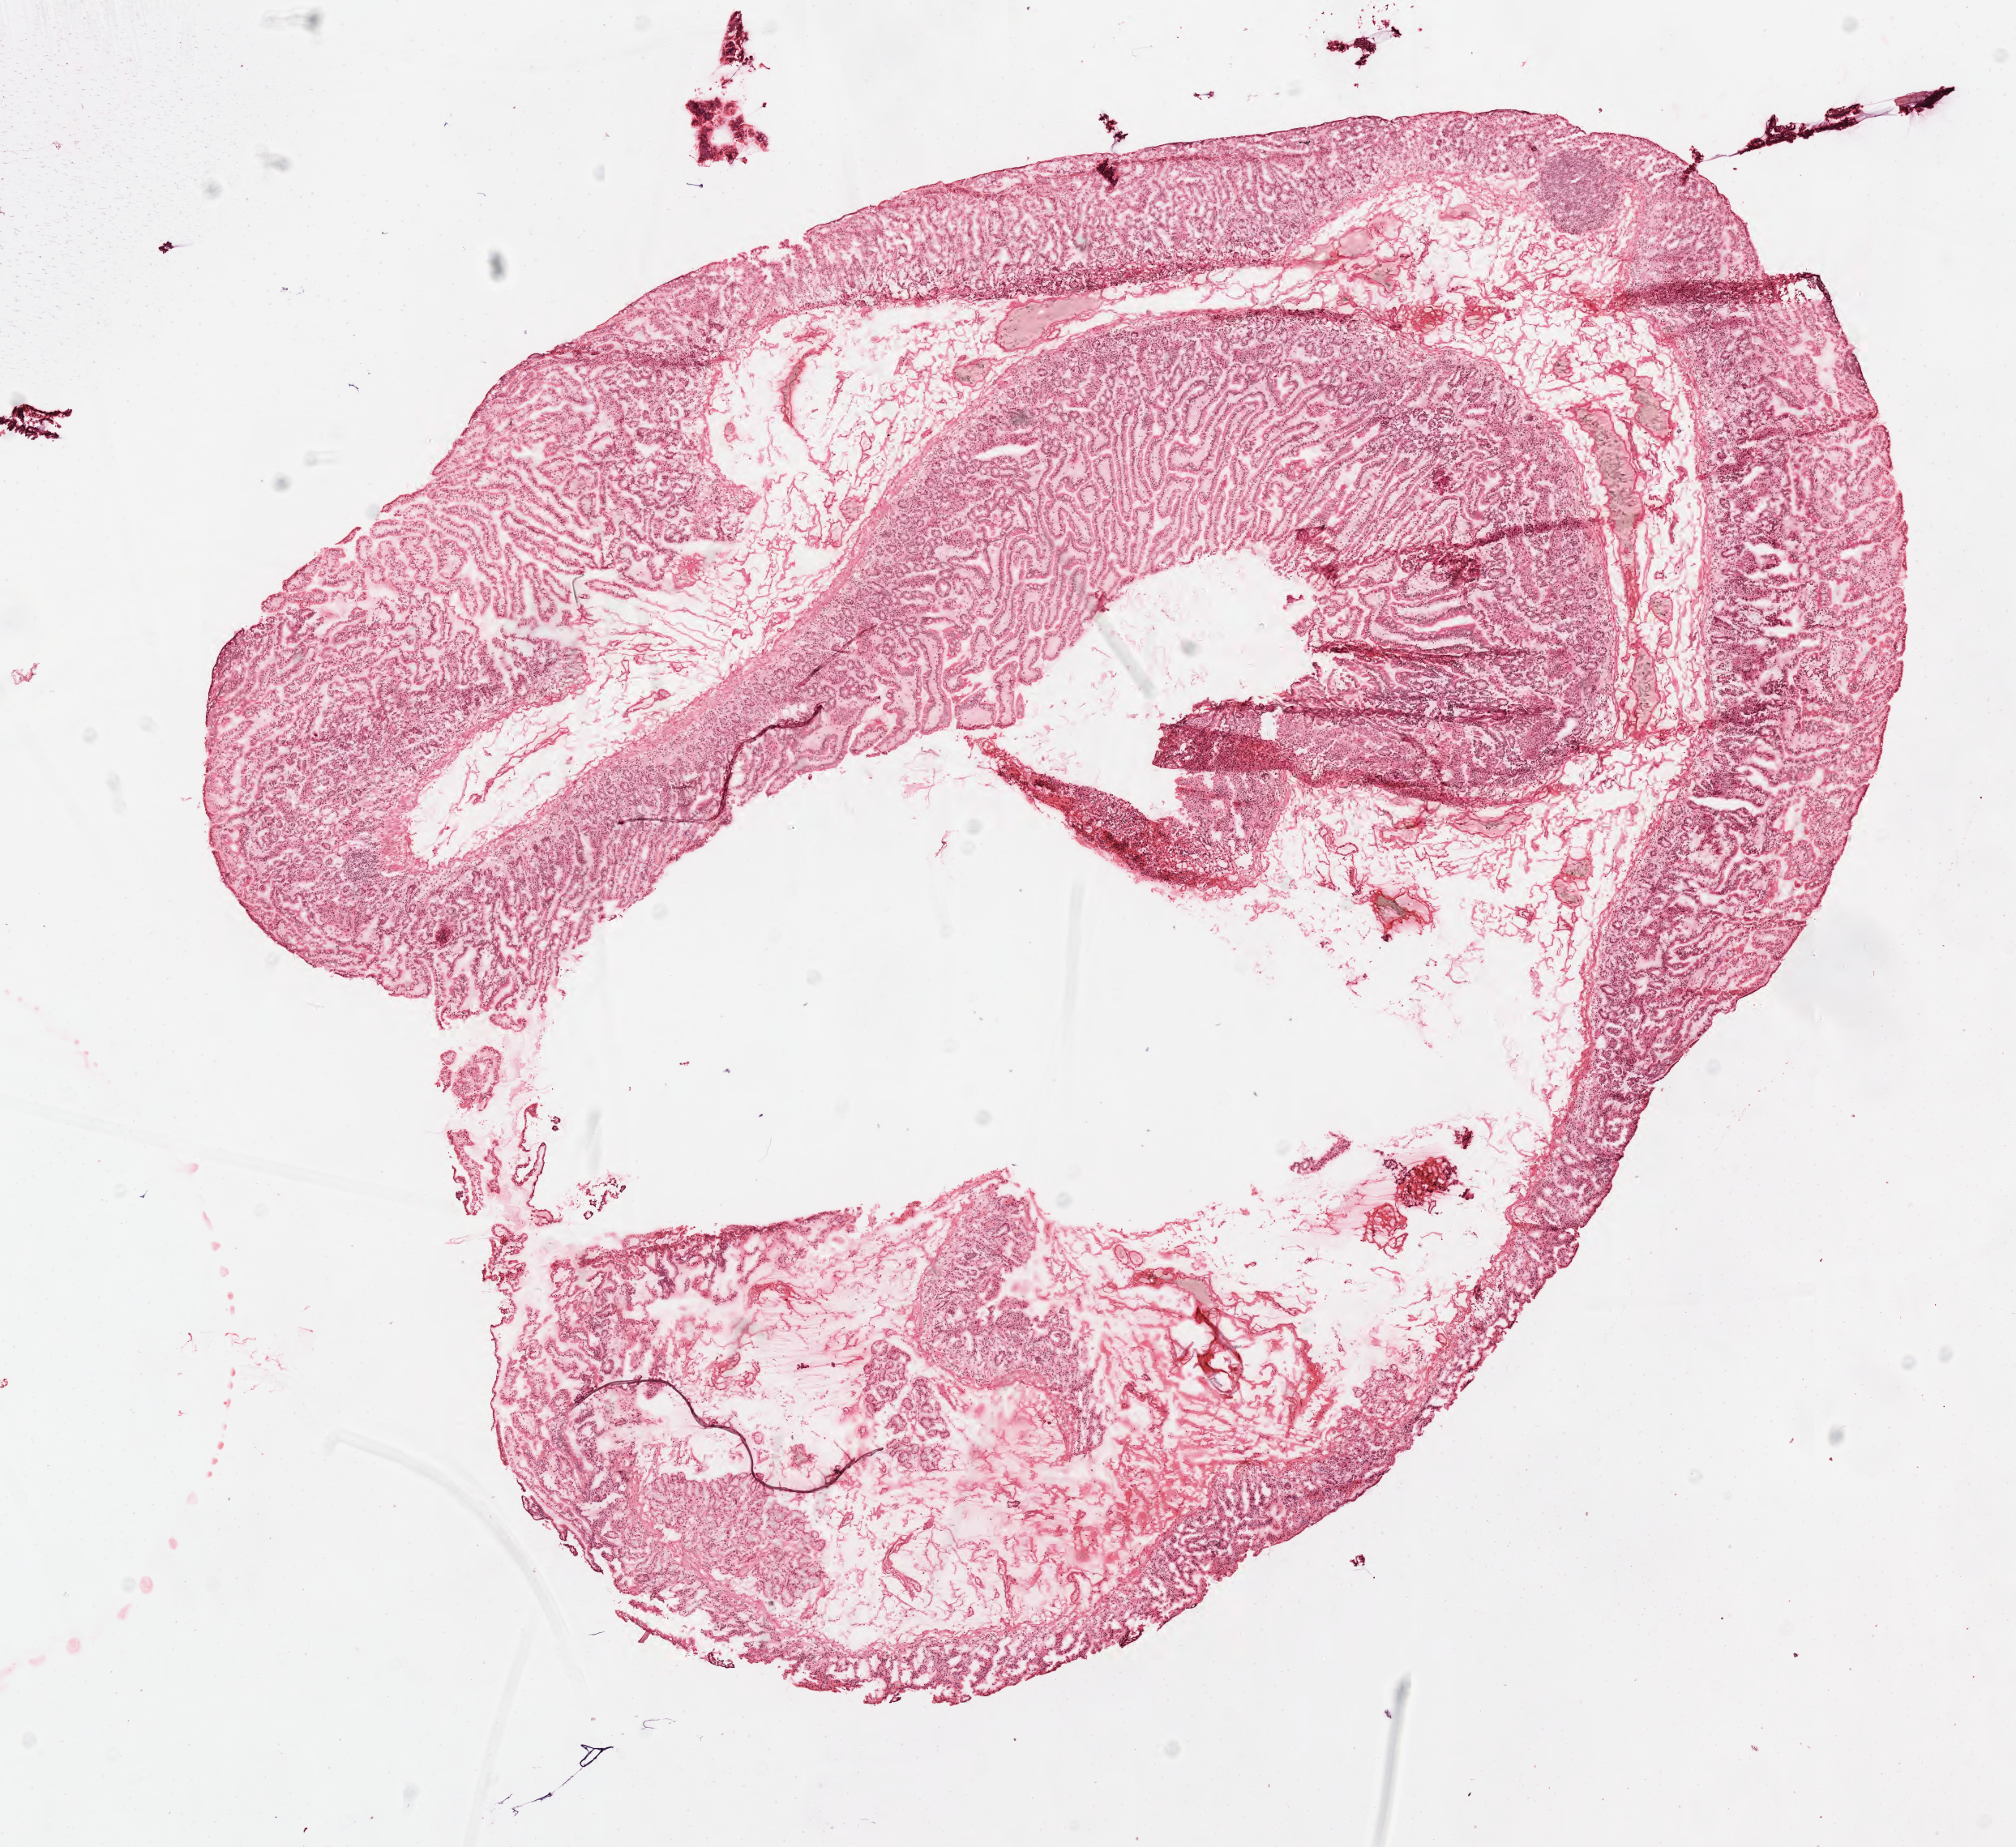
Whole-slide image, H&E stain — shown as a low-resolution overview of the whole scanned area (about 9.8 x 9.0 mm). Cryosection. Normal-tissue sample (non-tumor) from a patient with infiltrating duct carcinoma, NOS. Site: head of pancreas. Male patient; age at initial diagnosis 63 years. Slide review estimates, as recorded: tumor cells 0%, tumor nuclei 0%, stromal cells 0%, necrosis 0%, normal cells 100%. Inflammatory infiltration, as recorded: lymphocyte infiltration 0%, monocyte infiltration 0%, neutrophil infiltration 0%.
This section: non-tumor tissue sample; the patient's diagnosis is given above. Section: top of the tissue portion.